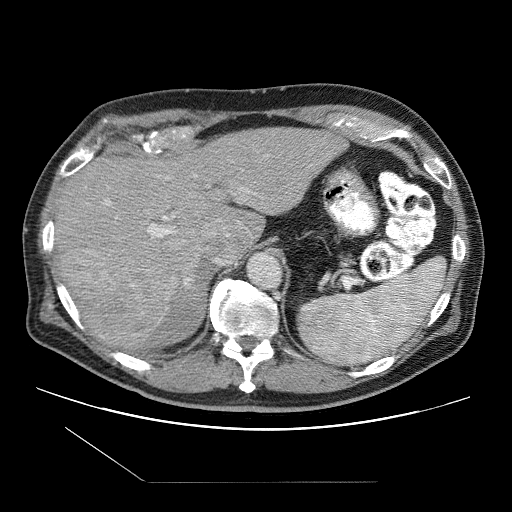
Contrast-enhanced abdominal CT (liver protocol), one axial slice; position 71 of 109 along the scan axis; 120 kVp; one of 2 acquisitions stored at this slice position; soft-tissue window (W 400 / L 40 HU); 2.5 mm slice thickness; 512 × 512 image matrix, field of view 400 × 400 mm. From the clinical record (not read from this slice): diagnosis: hepatocellular carcinoma (patient treated with transarterial chemoembolisation; whether this scan precedes or follows treatment is not stated here); TNM stage (as recorded): Stage-IIIB; Child-Pugh class: A; tumour differentiation: well differentiated; tumour nodularity: multinodular.
Outlined on this slice (semi-automatically segmented with operator editing):
- liver parenchyma outside the tumour (the mass and vessels are separate outlines, so this box may not span the whole liver): box from (x=54, y=128) to (x=348, y=348) px
- mass: (x=63, y=244)–(x=194, y=350)
- liver vessels: (x=105, y=189)–(x=255, y=281)